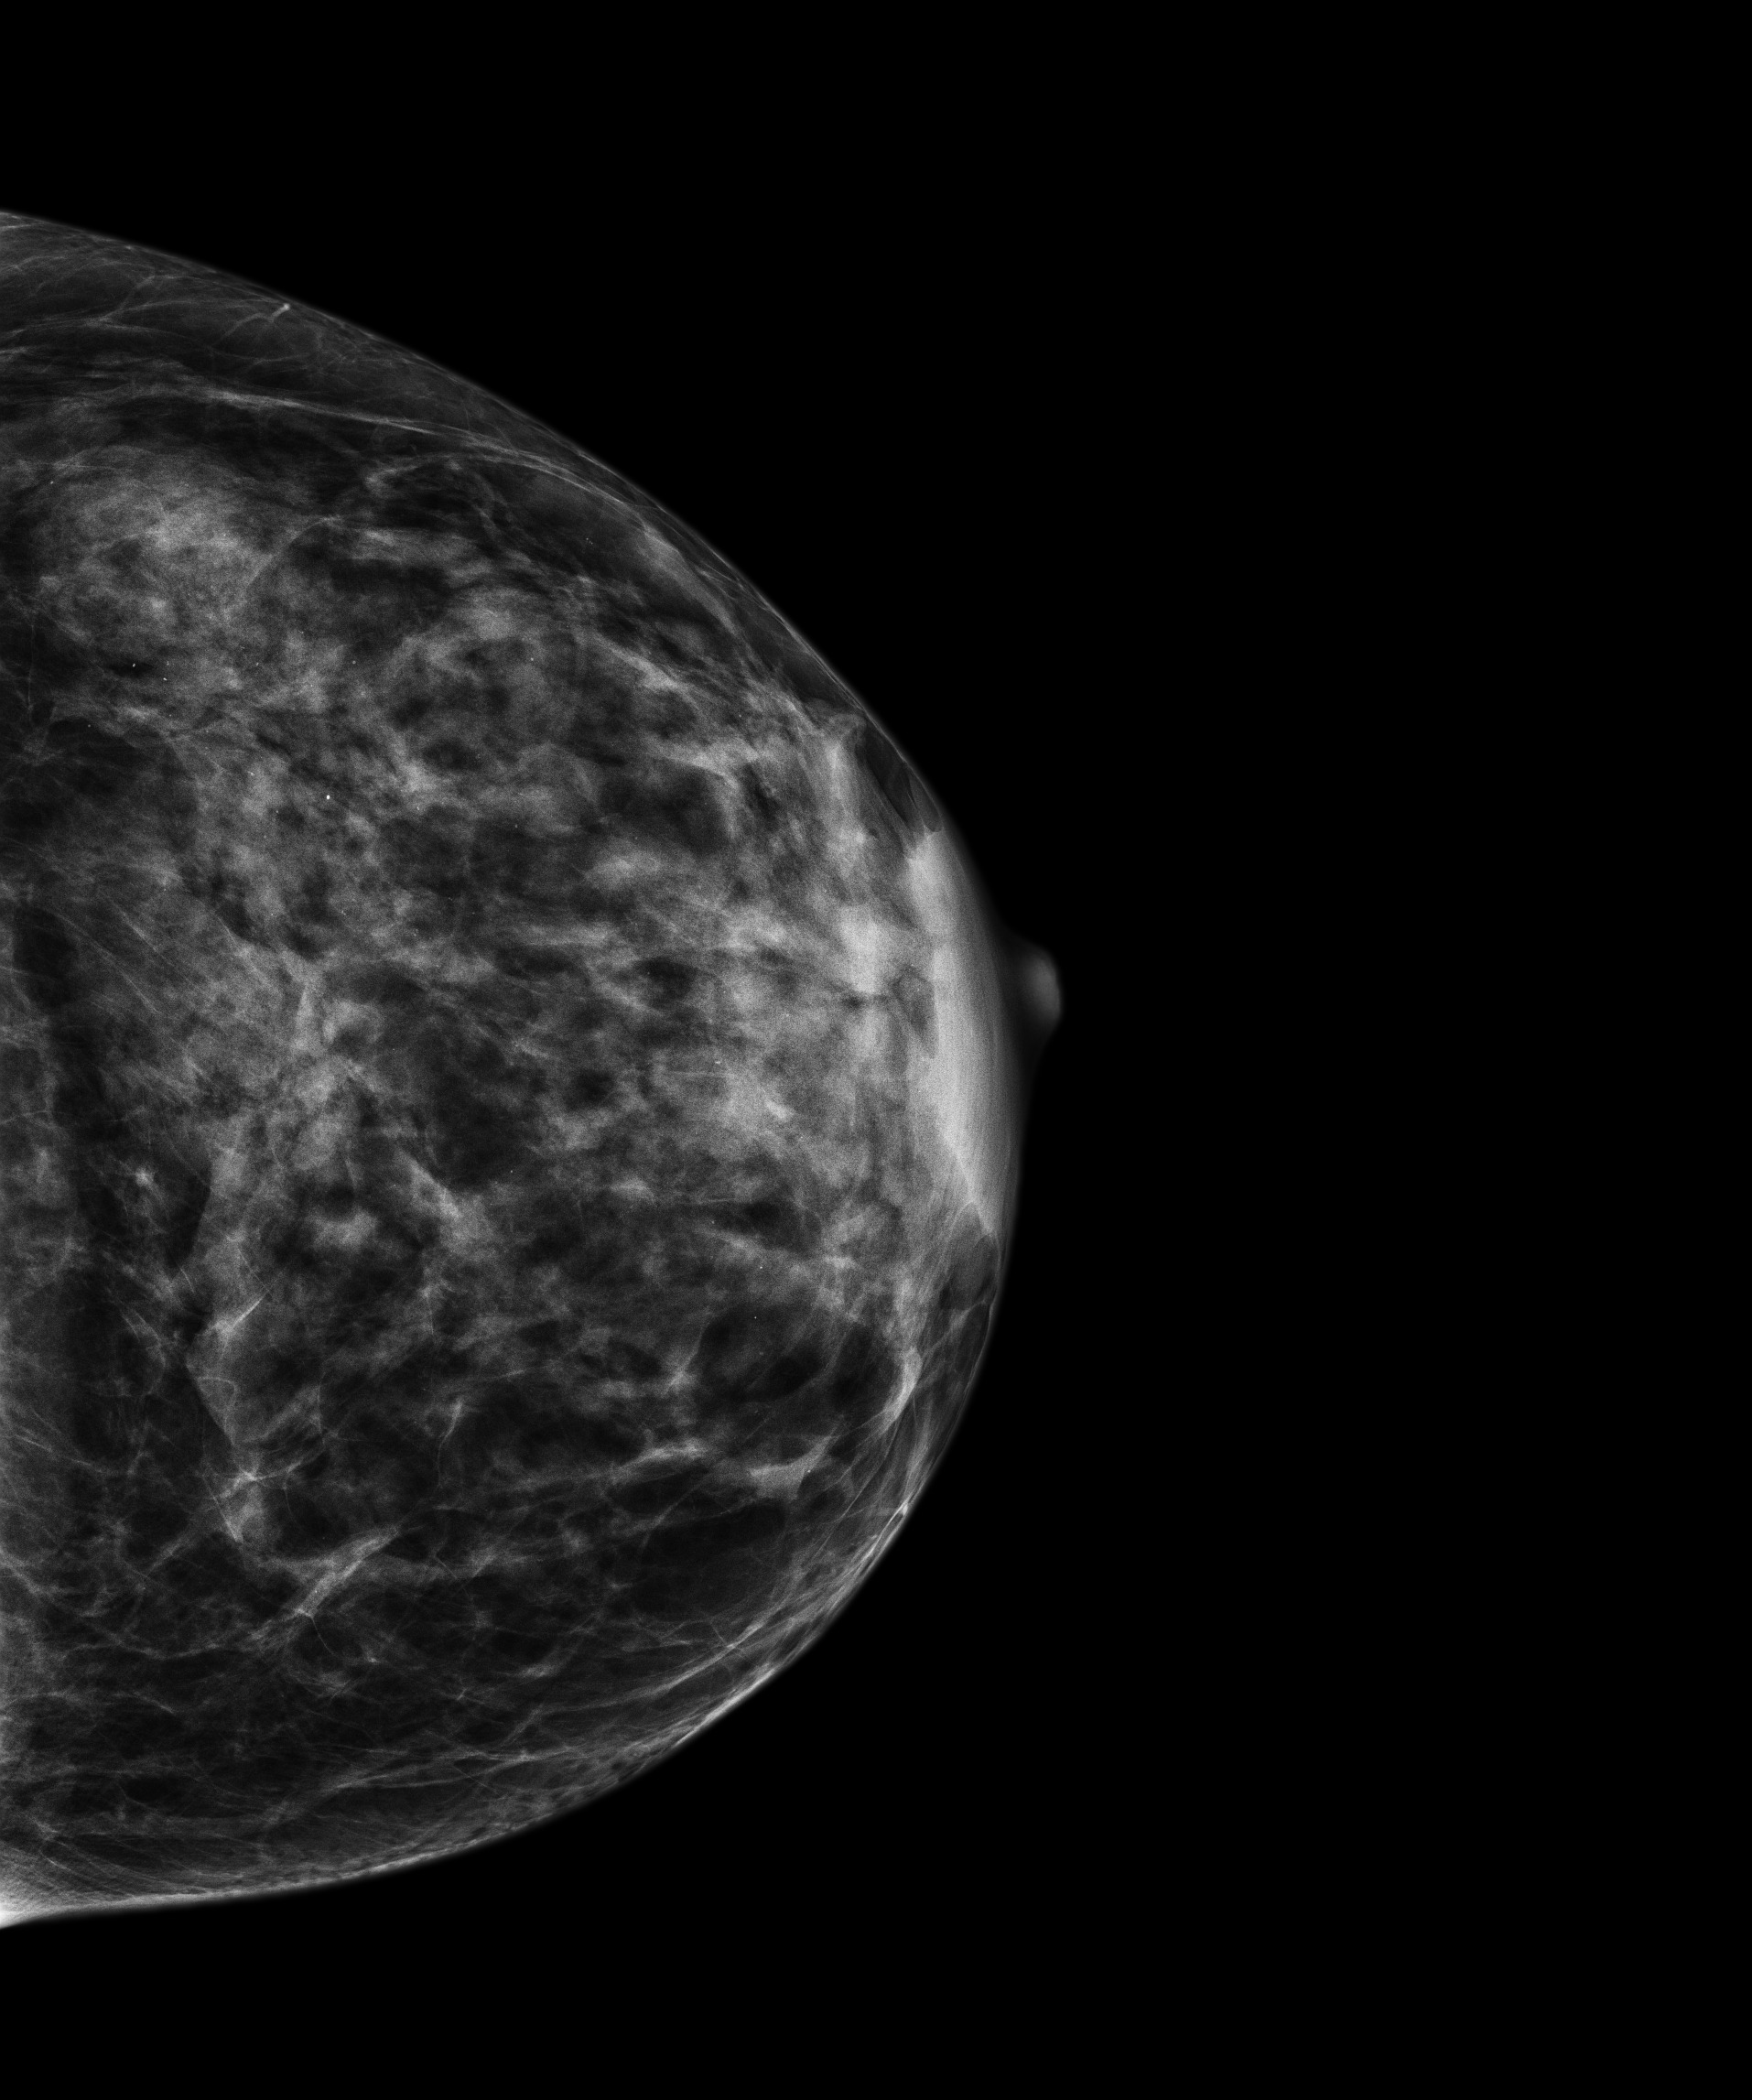
Diagnostic examination (additional views). Female patient, age 47 years.
Image type: full-field digital mammogram. Breast: left. Projection: cranio-caudal projection.